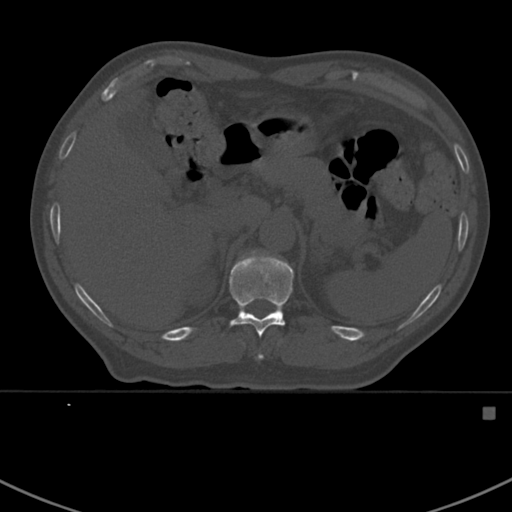
CT including the spine, one axial slice; position 347 of 412 along the scan axis; reconstruction kernel Br40s; bone window (W 1800 / L 400 HU); 1.5 mm slice thickness; 512 × 512 image matrix, field of view 358 × 358 mm. Male patient, age 59 years. Case-level facts recorded for this patient, not image findings: primary cancer: prostate.
Outlined on this slice (semi-automatically segmented with operator editing):
- T10 vertebra: bounding box (x1, y1, x2, y2) in pixels: (258, 355, 263, 359)
- T11 vertebra: (228, 250, 295, 338)